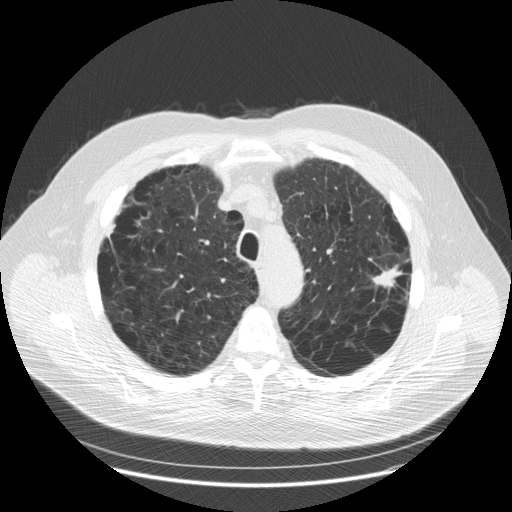
Low-dose screening chest CT, one axial slice. Position 137 of 179 along the scan axis. Lung window (W 1500 / L -600 HU). 2.5 mm slice thickness. 512 × 512 image matrix.
Structures marked on this image (manually delineated by an expert):
- lesion 1 (tumor, upper lobe of left lung): bounding box (x1, y1, x2, y2) in pixels: (372, 265, 403, 292)